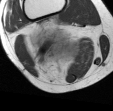
MRI of an extremity soft-tissue mass, one axial slice. Position 35 of 45 along the scan axis. MR volume resampled by the dataset authors to the PET/CT grid (not the native acquisition matrix). 3.27 mm slice thickness. 113 × 111 image matrix, field of view 110 × 108 mm. Female patient. Case-level facts recorded for this patient, not image findings: histological type: liposarcoma; site of the primary tumour: right thigh.
Outlined on this slice (expert contour drawn on MRI and transferred to this co-registered scan by the dataset authors):
- gross tumour volume (mass): bounding box <28,26,82,66> (left, top, right, bottom; pixels)